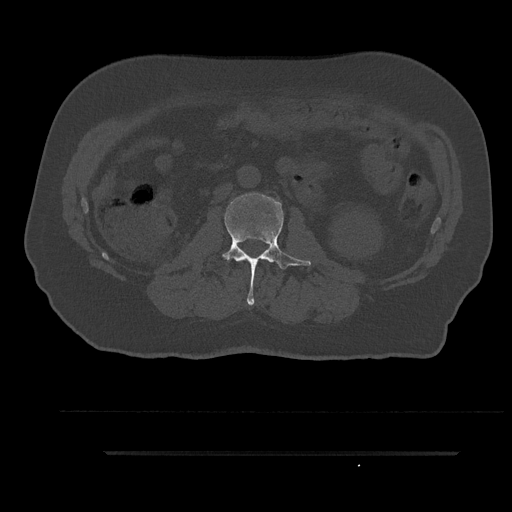
CT including the spine, one axial slice. Slice 106 of 797 in the series (ordered by position). 120 kVp. Bone window (W 1800 / L 400 HU). 0.5 mm slice thickness. 512 × 512 image matrix, field of view 432 × 432 mm. Patient: male, 63 years. From the clinical record (not read from this slice): primary cancer: renal; vertebrae with lytic lesions (as recorded): T8.
Structures marked on this image (semi-automatically segmented with operator editing):
- L2 vertebra: box from (x=222, y=193) to (x=311, y=305) px